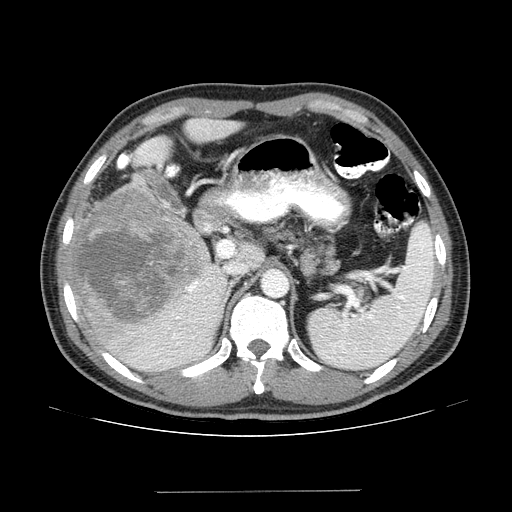
Contrast-enhanced abdominal CT (liver protocol), one axial slice; position 88 of 131 along the scan axis; 100 kVp; one of 2 acquisitions stored at this slice position; soft-tissue window (W 400 / L 40 HU); 2.5 mm slice thickness; 512 × 512 image matrix, field of view 380 × 380 mm. From the clinical record (not read from this slice): diagnosis: hepatocellular carcinoma (patient treated with transarterial chemoembolisation; whether this scan precedes or follows treatment is not stated here); TNM stage (as recorded): Stage-I; Child-Pugh class: A; tumour differentiation: poorly differentiated; tumour size: 10.3 cm.
Outlined on this slice (semi-automatic segmentation, software-assisted and operator-edited):
- liver parenchyma outside the tumour (the mass and vessels are separate outlines, so this box may not span the whole liver): bounding box (x1, y1, x2, y2) in pixels: (64, 118, 241, 372)
- mass: (68, 187, 208, 327)
- liver vessels: (151, 284, 215, 363)